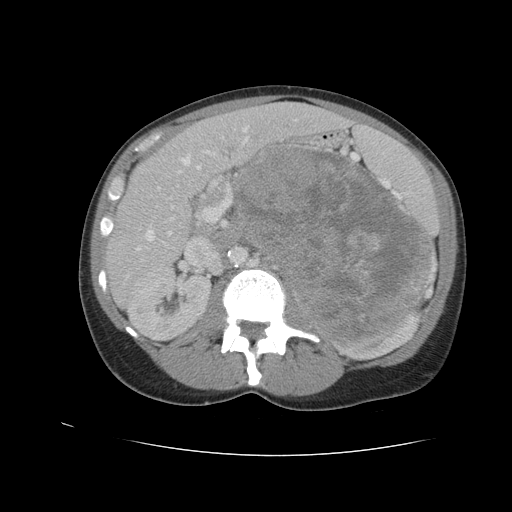
Contrast-enhanced abdominal CT, one axial slice; reconstruction kernel STANDARD; soft-tissue window (W 400 / L 40 HU); 5 mm slice thickness; 512 × 512 image matrix, field of view 360 × 360 mm. Female patient. Case-level facts recorded for this patient, not image findings: diagnosis: adrenocortical carcinoma; tumour side: left adrenal; tumour size at pathology: 18 cm; Ki-67 index: 11 %; stage (as recorded): 3.
Outlined on this slice (semi-automatically segmented with operator editing):
- mass: box from (x=235, y=147) to (x=431, y=343) px